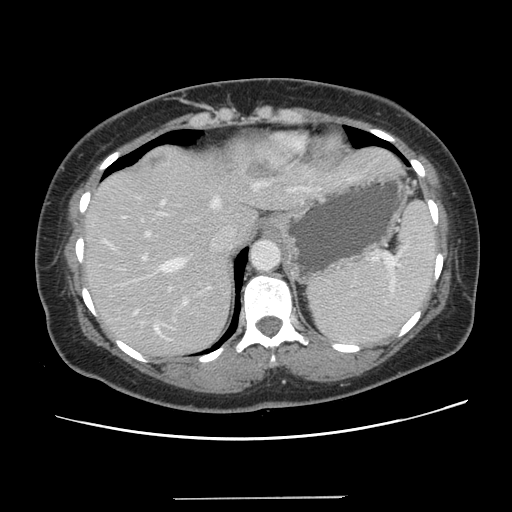
Contrast-enhanced abdominal CT, one axial slice; position 102 of 141 along the scan axis; intravenous contrast given; soft-tissue window (W 400 / L 40 HU); 2.5 mm slice thickness; 512 × 512 image matrix, field of view 366 × 366 mm. Female patient, age 53 years. Case-level facts recorded for this patient, not image findings: diagnosis: colorectal cancer liver metastases, imaged before liver resection; multiple liver metastases: no; largest metastasis: 14.5 cm; chemotherapy before resection: yes.
Annotated regions visible in this slice (manually delineated by an expert):
- hepatic veins: bounding box [x1, y1, x2, y2] px = [107, 179, 271, 332]
- liver: [85, 145, 400, 357]
- planned liver remnant (the part of the liver to remain after resection): [85, 209, 259, 357]
- portal vein (with intrahepatic branches): [122, 188, 295, 321]
- liver metastasis: [148, 155, 162, 168]